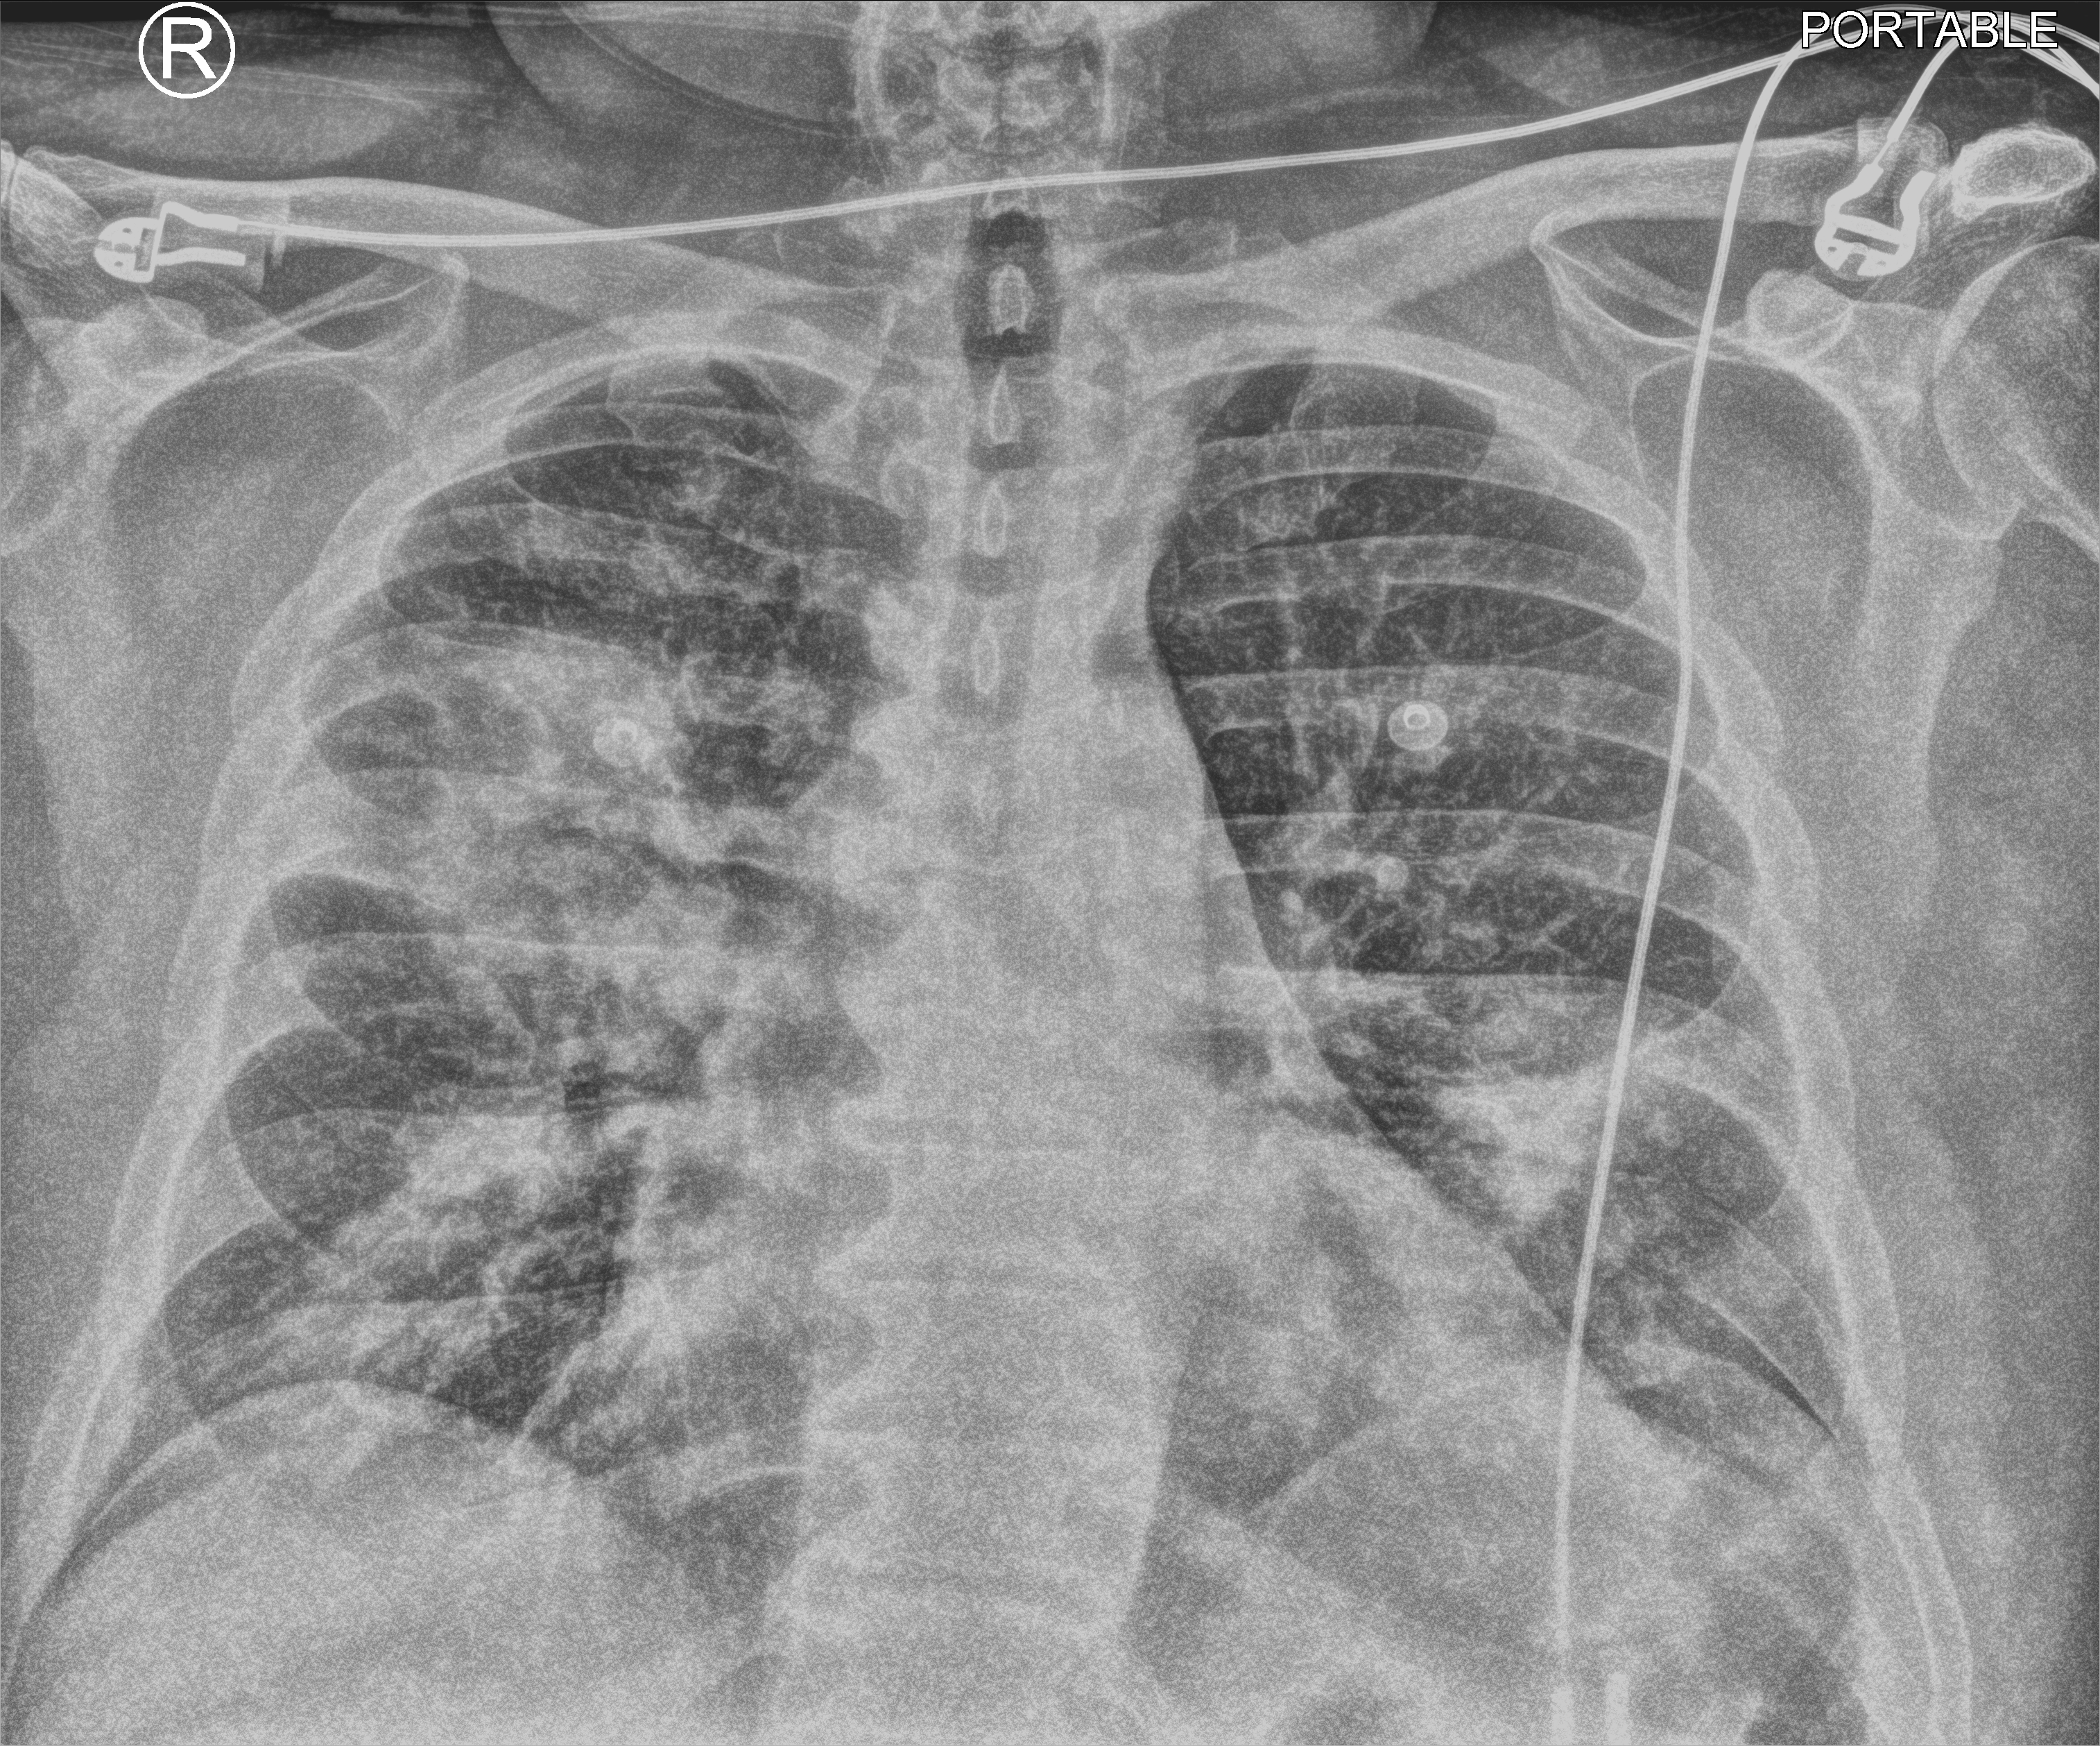
Chest X-ray (portable), anteroposterior (AP) projection. Male patient hospitalised with COVID-19, age 18–59 years.
Admission-level facts for this patient (not findings on this image; timing relative to this image not recorded):
- admitted to intensive care during this hospital stay: no
- mechanically ventilated during this hospital stay: no